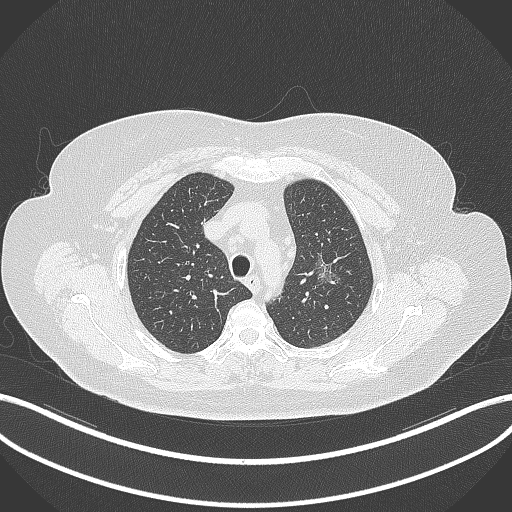
Chest CT, one axial slice; position 264 of 309 along the scan axis; reconstruction kernel B70f; lung window (W 1500 / L -600 HU); 1 mm slice thickness; 512 × 512 image matrix, field of view 400 × 400 mm. Female patient, age 70 years. From the clinical record (not read from this slice): clinical TNM (as recorded): T1c N0 M0.
Annotated regions visible in this slice (rectangle marked by the reading radiologist):
- lung tumour (recorded histology: adenocarcinoma): bounding box (x1, y1, x2, y2) in pixels: (308, 253, 341, 294)